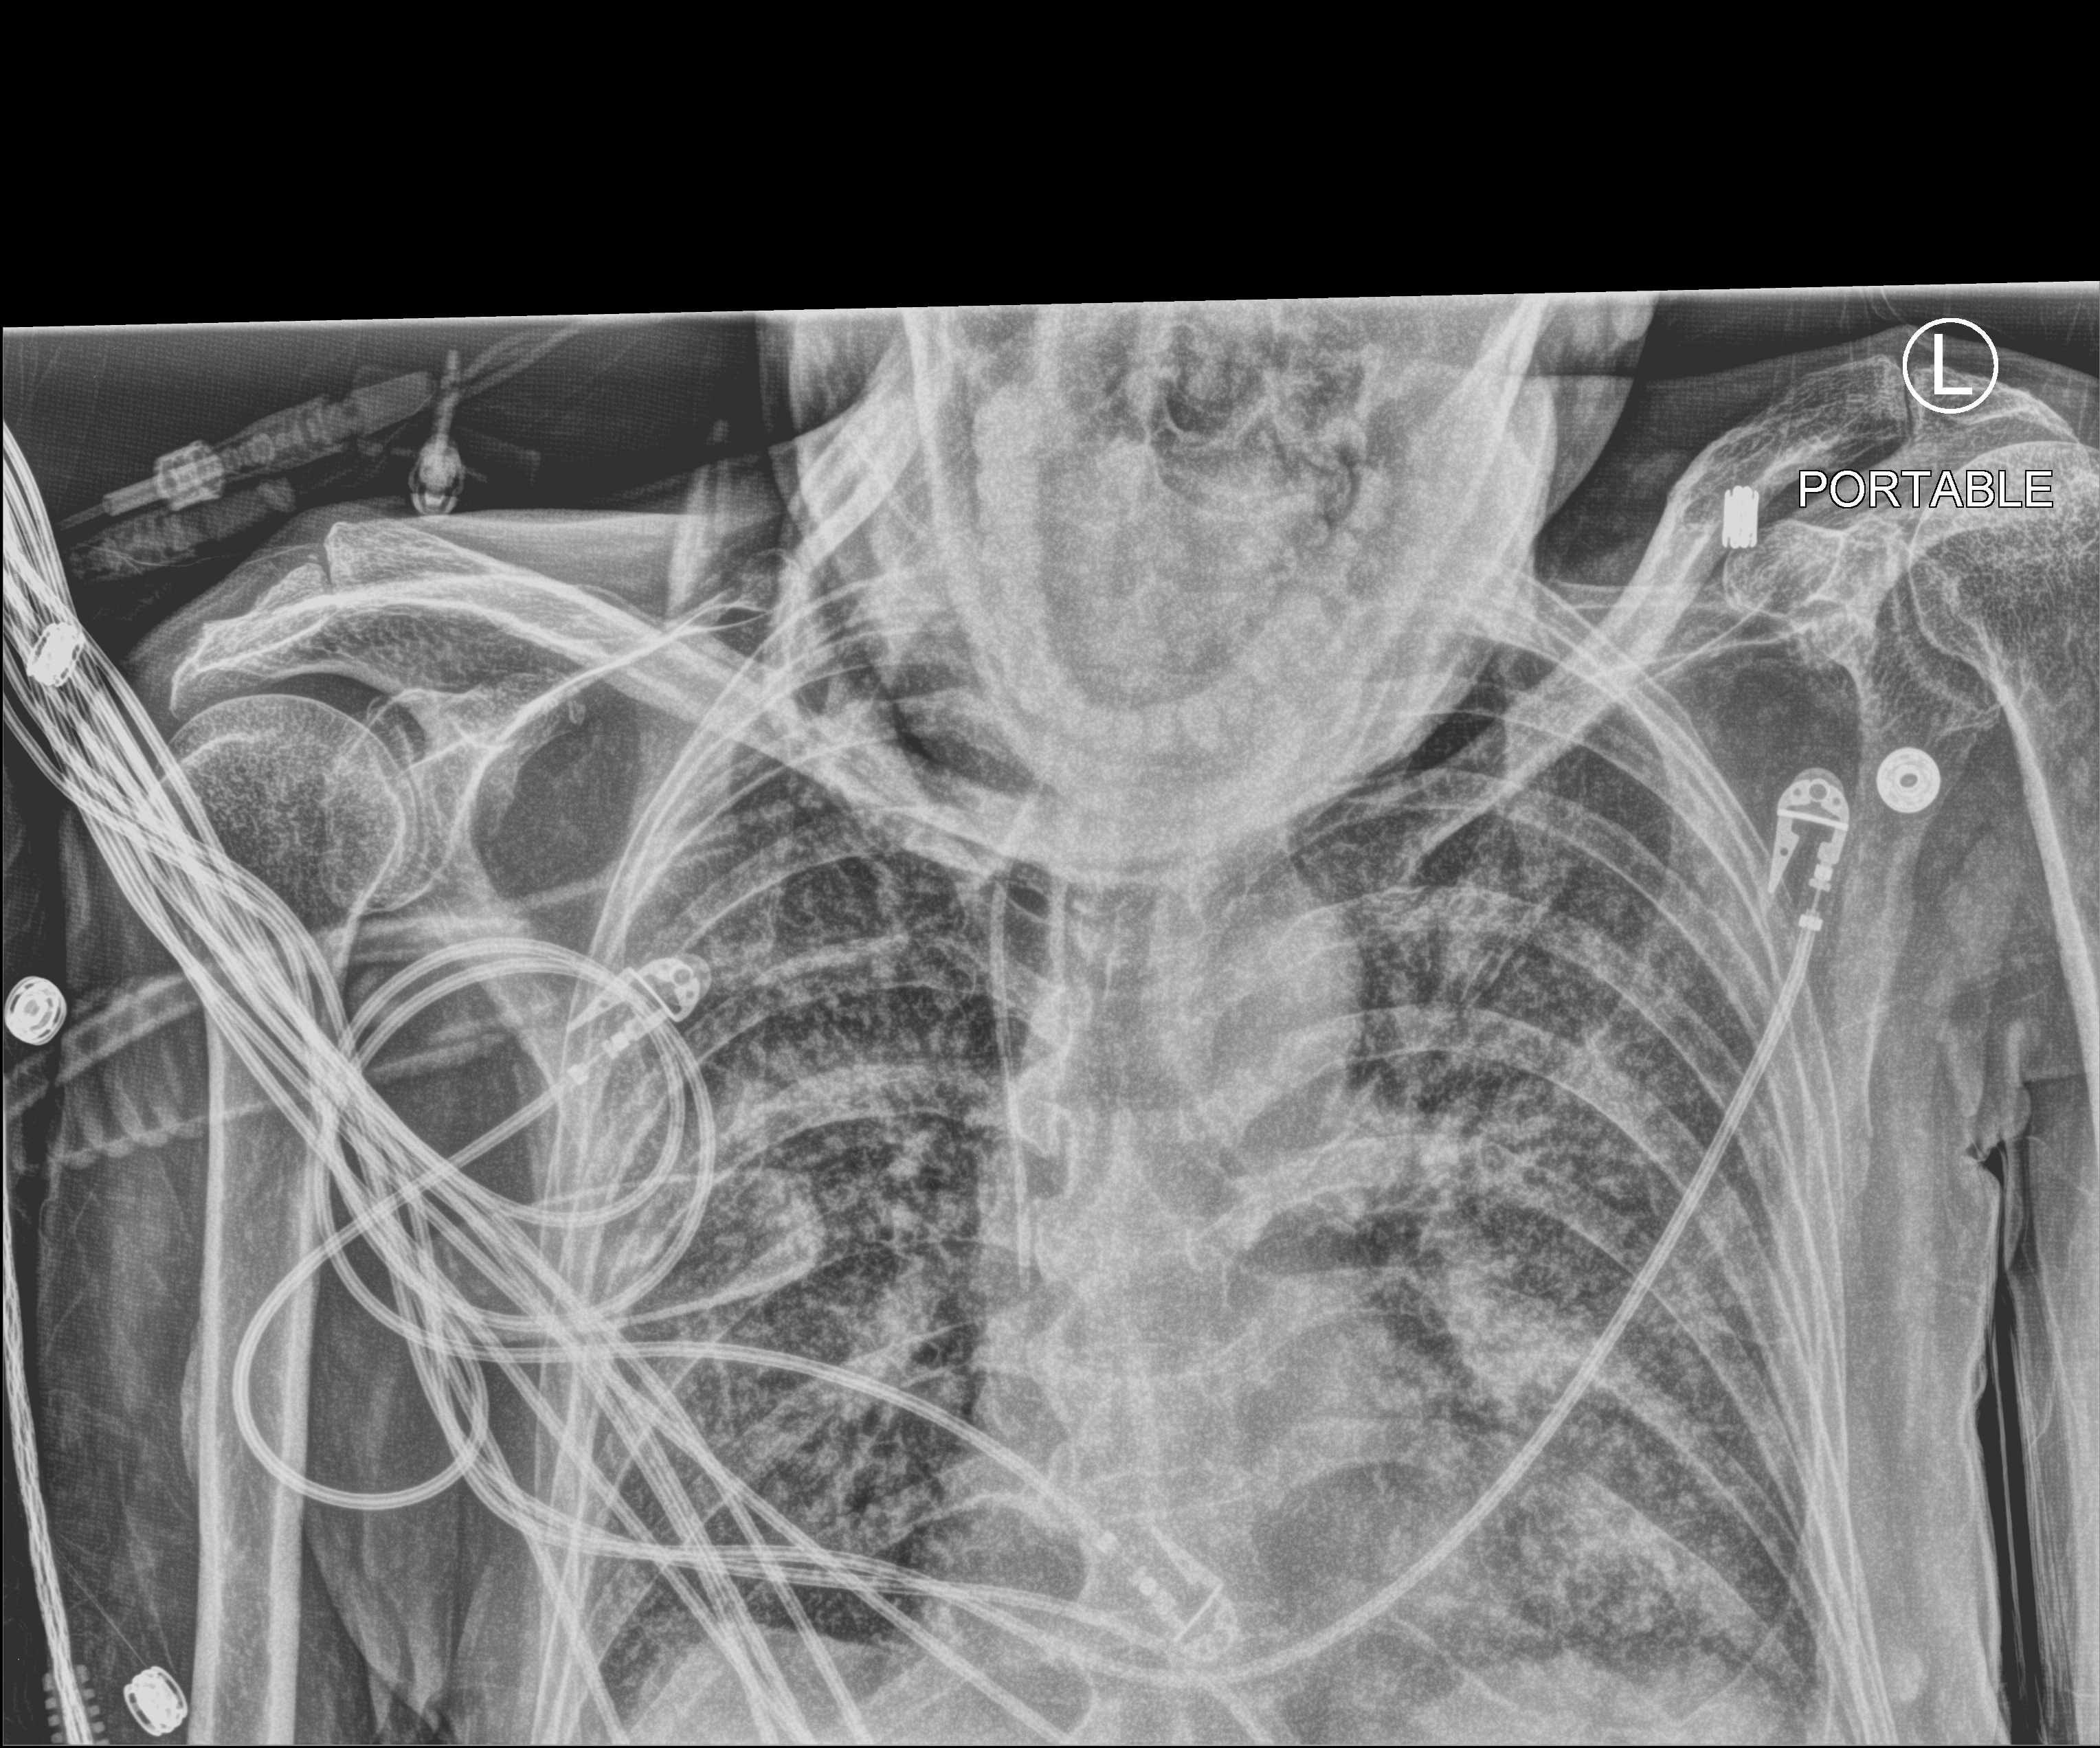
Chest X-ray (portable), anteroposterior (AP) projection. Male patient hospitalised with COVID-19, age 60–74 years.
Admission-level facts for this patient (not findings on this image; timing relative to this image not recorded):
- admitted to intensive care during this hospital stay: yes
- mechanically ventilated during this hospital stay: yes